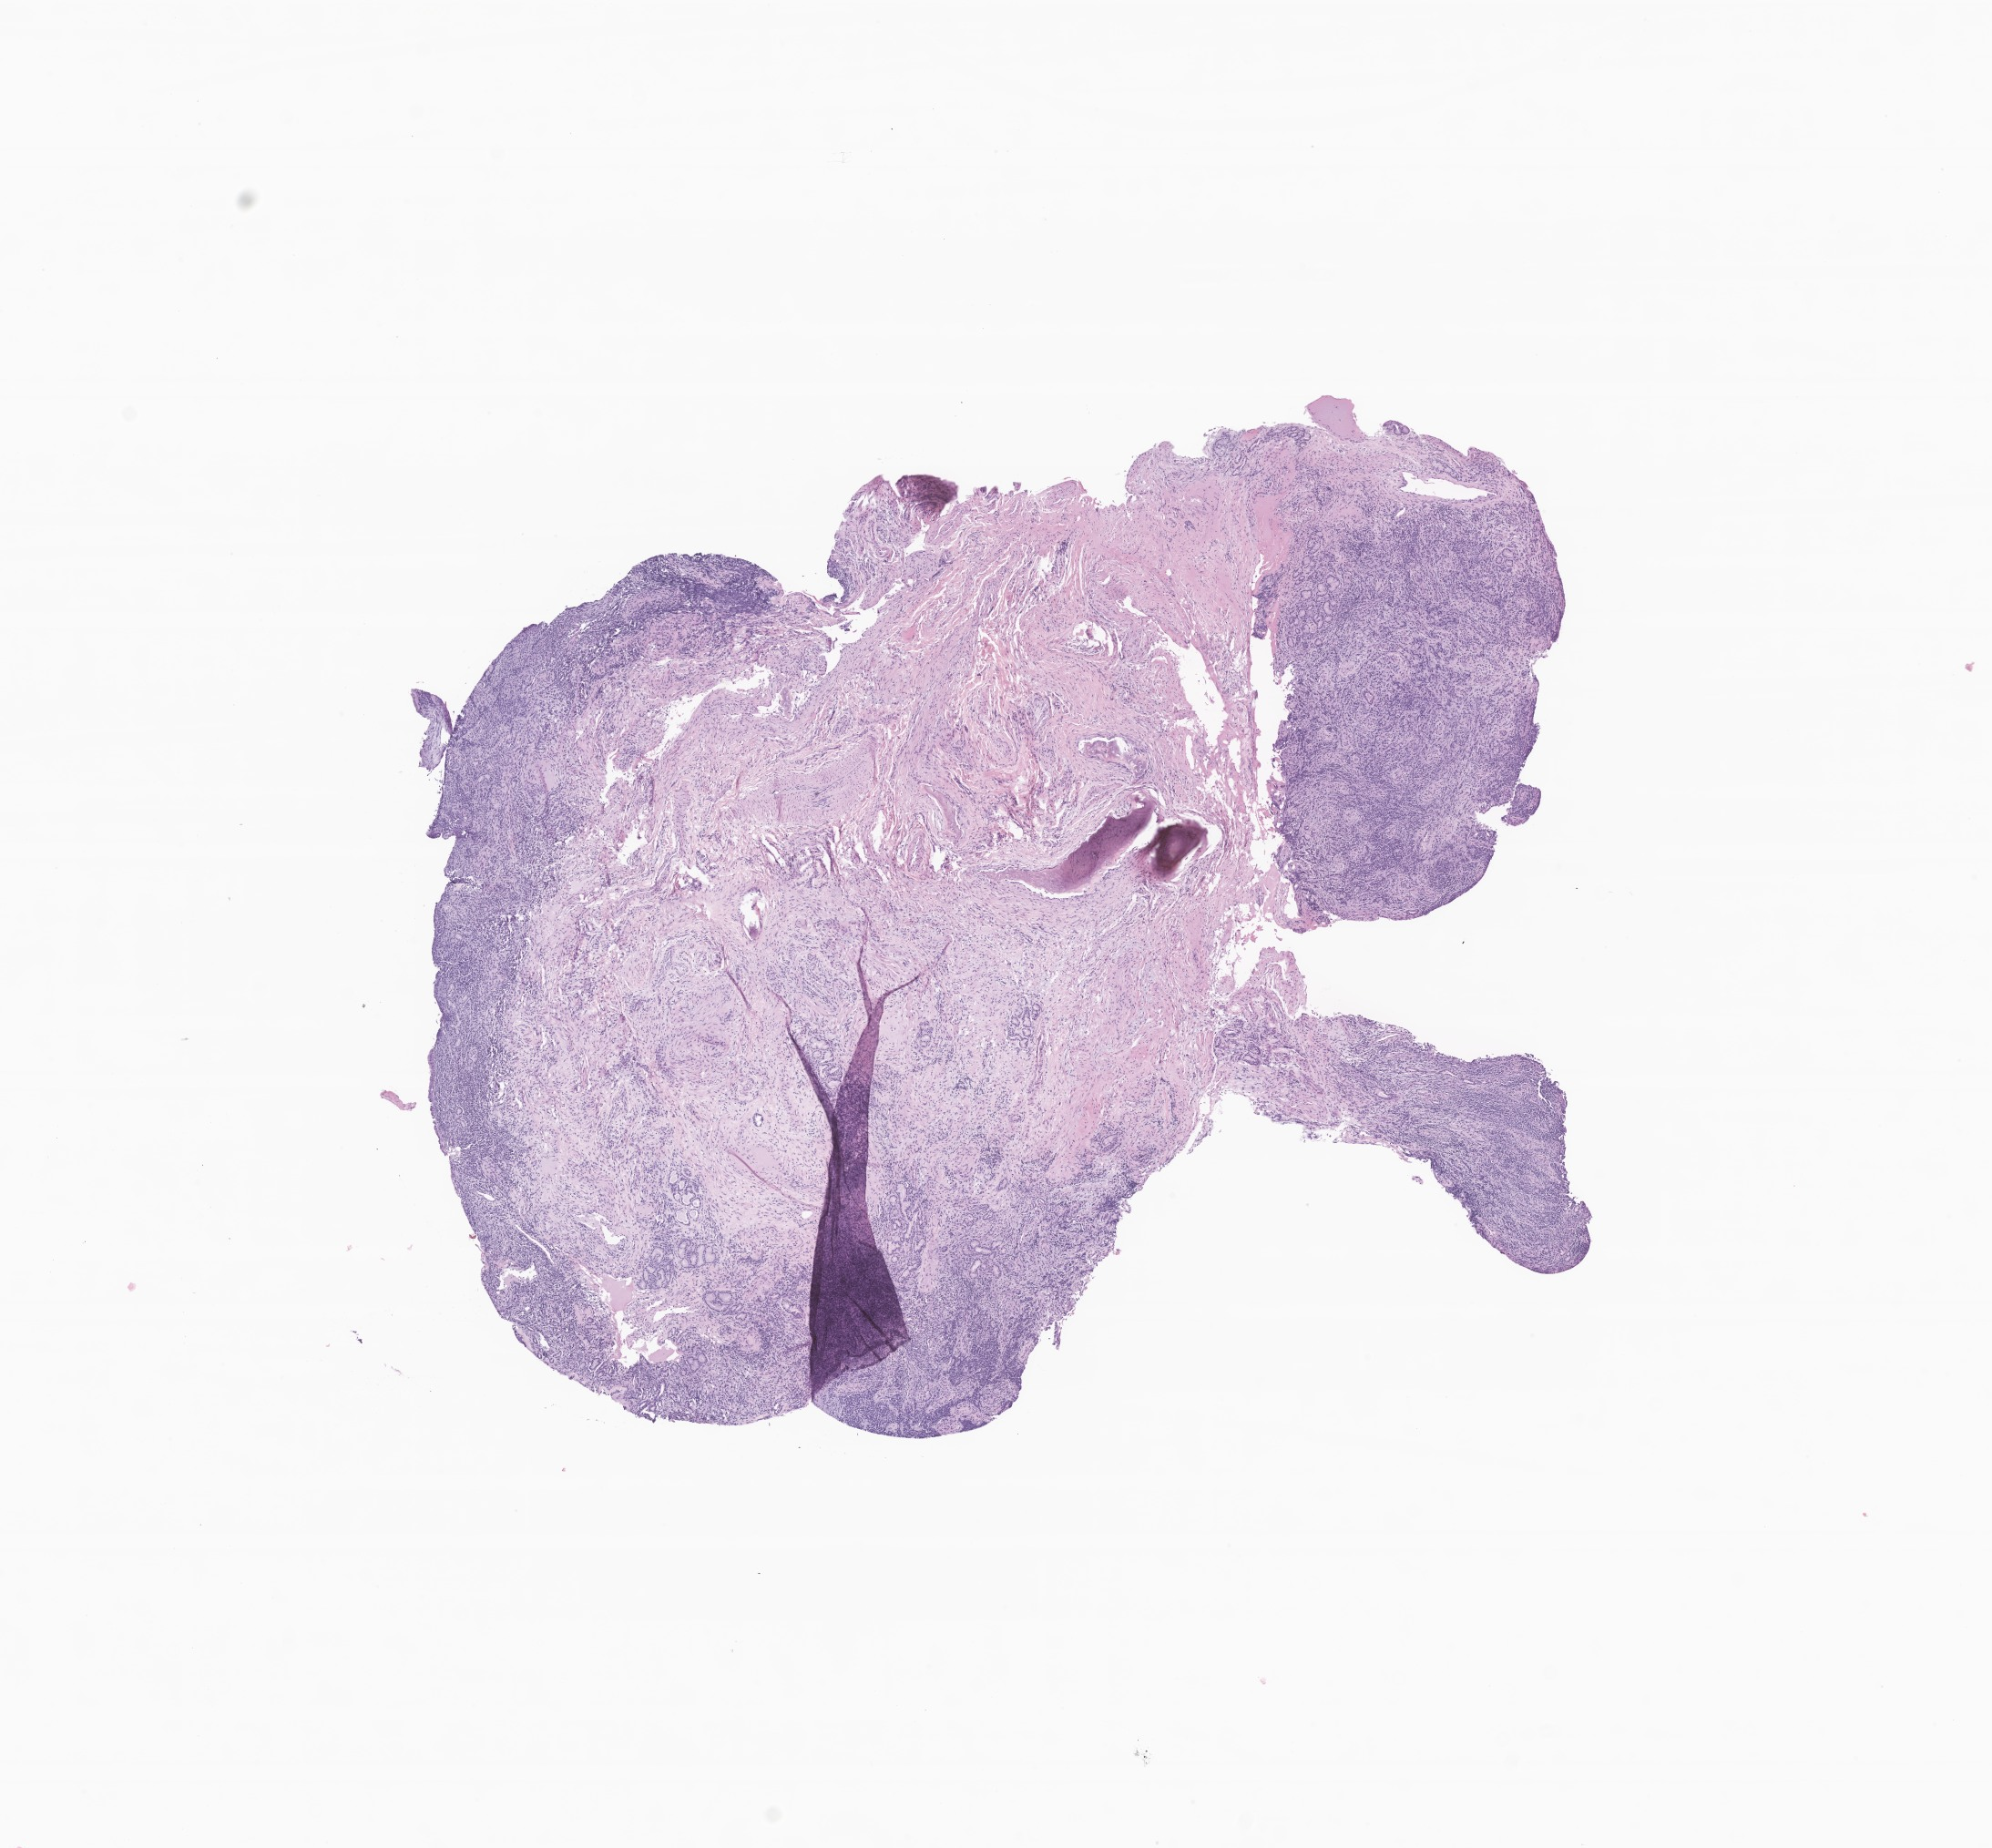
Digitized H&E-stained section of tumor tissue from the maxillary sinus, low-resolution overview of the scanned area, about 9.2 x 8.6 mm, FFPE section. Patient: male, age 235 months (19 years 7 months).
Diagnosis: Rhabdomyosarcoma, NOS.